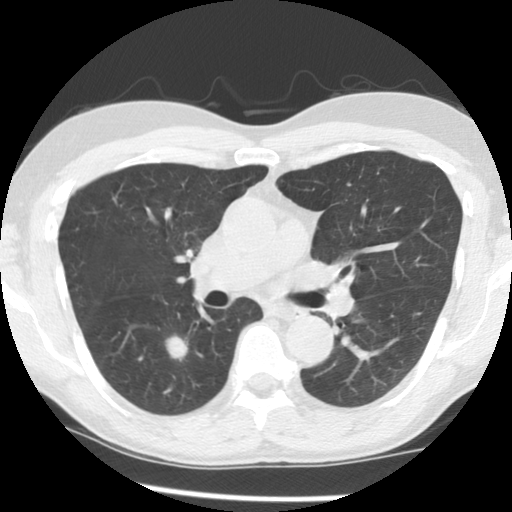
Chest CT (low-dose screening protocol), one axial image; third screening round (two years after baseline); lung window (W 1500 / L -600 HU); standard (soft-tissue) reconstruction kernel (STANDARD); 140 kVp. Male participant, aged 65 years at enrolment. Current smoker at enrolment.
- Expert reader's lesion annotation, box from (x=148, y=322) to (x=209, y=377) px.
- The screening reader recorded 2 non-calcified nodules or masses ≥4 mm on this exam (left lower lobe, right lower lobe); which of them this box marks is not recorded.